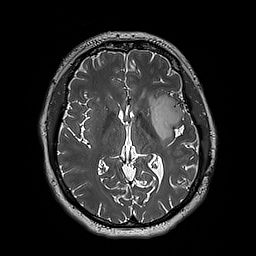
Brain MRI from a brain-tumour surgery series, one axial slice. 256 × 256 image matrix, field of view 250 × 250 mm. Case-level facts recorded for this patient, not image findings: histopathology: Astrocytoma; WHO grade: 3; IDH mutation: yes.
Outlined on this slice (expert manual segmentation):
- tumour: box from (x=148, y=96) to (x=184, y=141) px